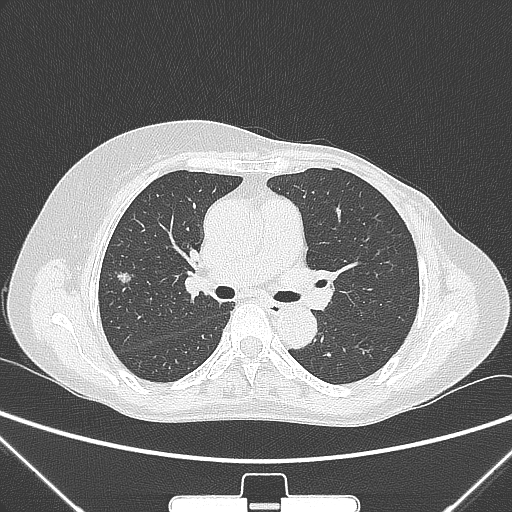
Chest CT, one axial slice. Position 152 of 265 along the scan axis. 120 kVp. Lung window (W 1500 / L -600 HU). 1 mm slice thickness. 512 × 512 image matrix. Female patient, age 64 years. Case-level facts recorded for this patient, not image findings: clinical TNM (as recorded): T1c N0 M0.
Outlined on this slice (rectangle marked by the reading radiologist):
- lung tumour (recorded histology: adenocarcinoma): bounding box <114,265,142,289> (left, top, right, bottom; pixels)